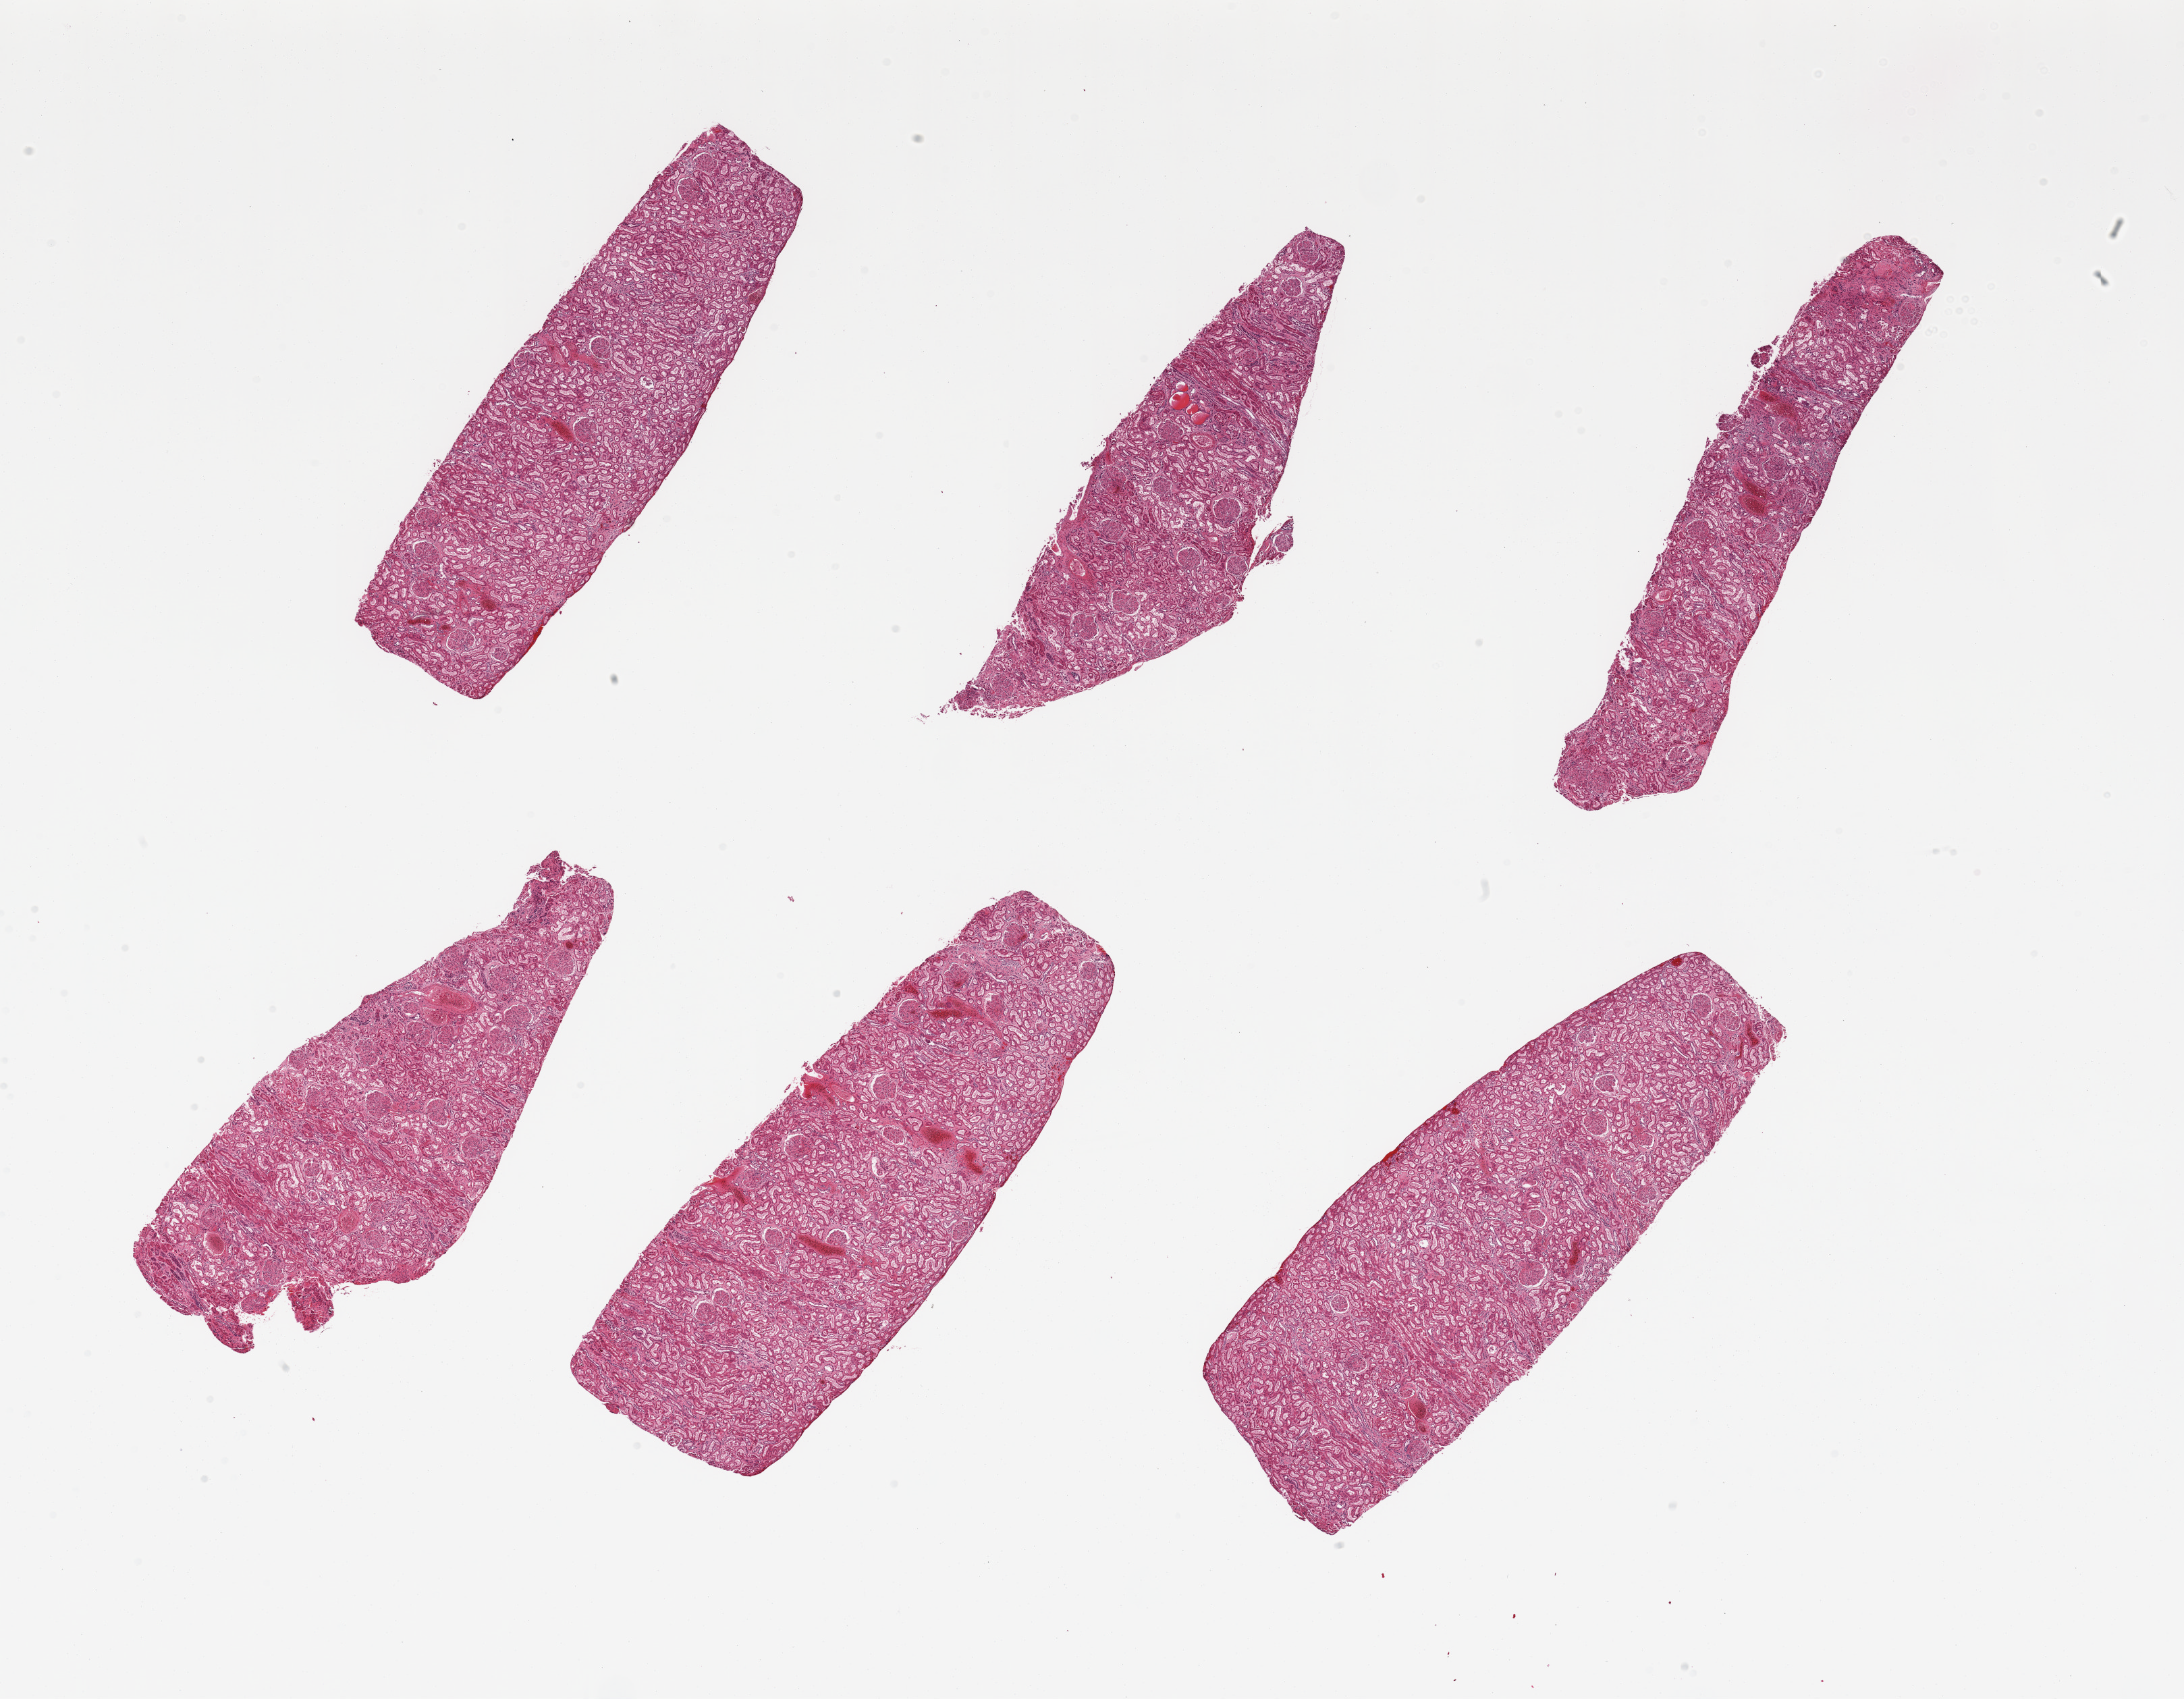
Whole-slide image, H&E stain, whole scanned area (about 25.6 x 19.9 mm, slide scanned at 20x) shown as a low-resolution overview; PAXgene-fixed paraffin-embedded (PFPE) section; target tissue: renal cortex; tissue donor sample. Male donor.
• pathologist's review note for this sample: 6 pieces, glomeruli present; tubules fairly well preserved